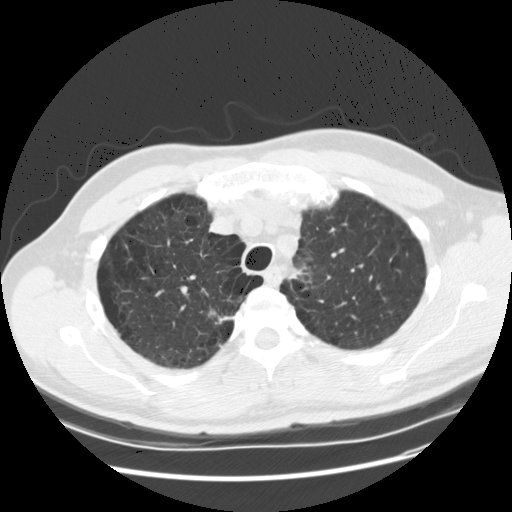
Axial slice from a low-dose chest CT screening exam. Baseline screening round. Lung window (W 1500 / L -600 HU). 2.5 mm slice thickness. Standard (soft-tissue) reconstruction kernel (STANDARD). Slice 29 of 132 in the series. 512 × 512 image matrix. Male, age 61 years at enrolment. Former smoker at enrolment.
Expert reader's lesion annotation, bounding box <189,288,242,340> (left, top, right, bottom; pixels). Screening reader's record for this exam (one nodule recorded; not confirmed to be the boxed lesion): non-calcified nodule or mass ≥4 mm, right upper lobe, 19 × 13 mm, poorly defined margins, soft tissue attenuation. Official screen result: positive, change unspecified: nodule(s) >= 4 mm or enlarging nodule(s), mass(es), or other non-specific abnormalities suspicious for lung cancer. Lung cancer was diagnosed 62 days after this screen: squamous cell carcinoma, NOS, right upper lobe, poorly differentiated (G3), stage IA (AJCC 6th edition), 20 mm at pathology.